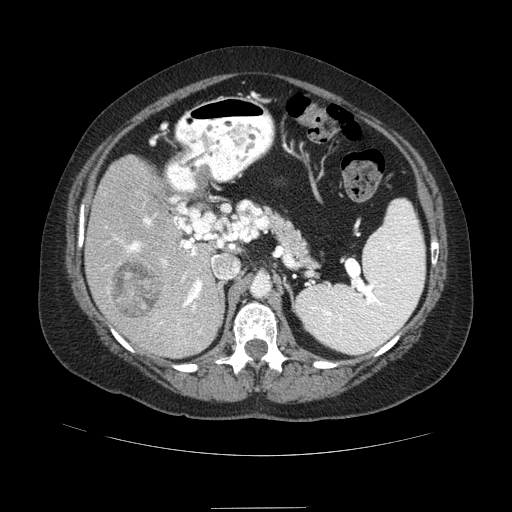
Contrast-enhanced abdominal CT (liver protocol), one axial slice; position 47 of 89 along the scan axis; reconstruction kernel STANDARD; soft-tissue window (W 400 / L 40 HU); 512 × 512 image matrix, field of view 400 × 400 mm. From the clinical record (not read from this slice): diagnosis: hepatocellular carcinoma (patient treated with transarterial chemoembolisation; whether this scan precedes or follows treatment is not stated here); TNM stage (as recorded): Stage-IIIB; Child-Pugh class: A; tumour nodularity: multinodular.
Annotated regions visible in this slice (semi-automatically segmented with operator editing):
- liver parenchyma outside the tumour (the mass and vessels are separate outlines, so this box may not span the whole liver): box from (x=84, y=154) to (x=224, y=358) px
- mass: (x=110, y=257)–(x=160, y=318)
- liver vessels: (x=115, y=197)–(x=219, y=333)